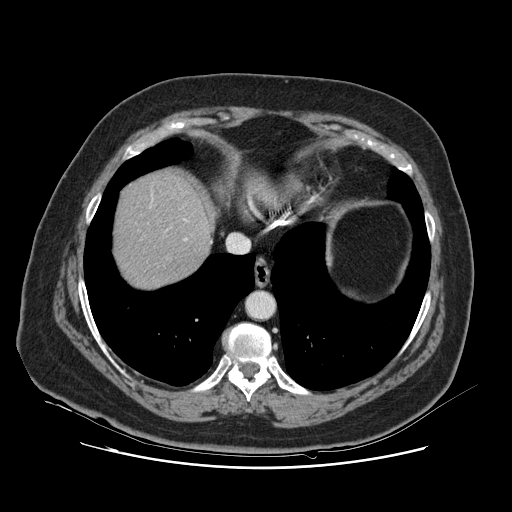
Contrast-enhanced abdominal CT, one axial slice; slice 110 of 132 in the series (ordered by position); 120 kVp; soft-tissue window (W 400 / L 40 HU); 2.5 mm slice thickness; 512 × 512 image matrix. Female patient, age 73 years. From the clinical record (not read from this slice): diagnosis: colorectal cancer liver metastases, imaged before liver resection; multiple liver metastases: no; largest metastasis: 7 cm.
Structures marked on this image (expert manual segmentation):
- hepatic veins: bounding box (x1, y1, x2, y2) in pixels: (150, 206, 187, 241)
- liver: (115, 174, 210, 287)
- planned liver remnant (the part of the liver to remain after resection): (116, 174, 209, 289)